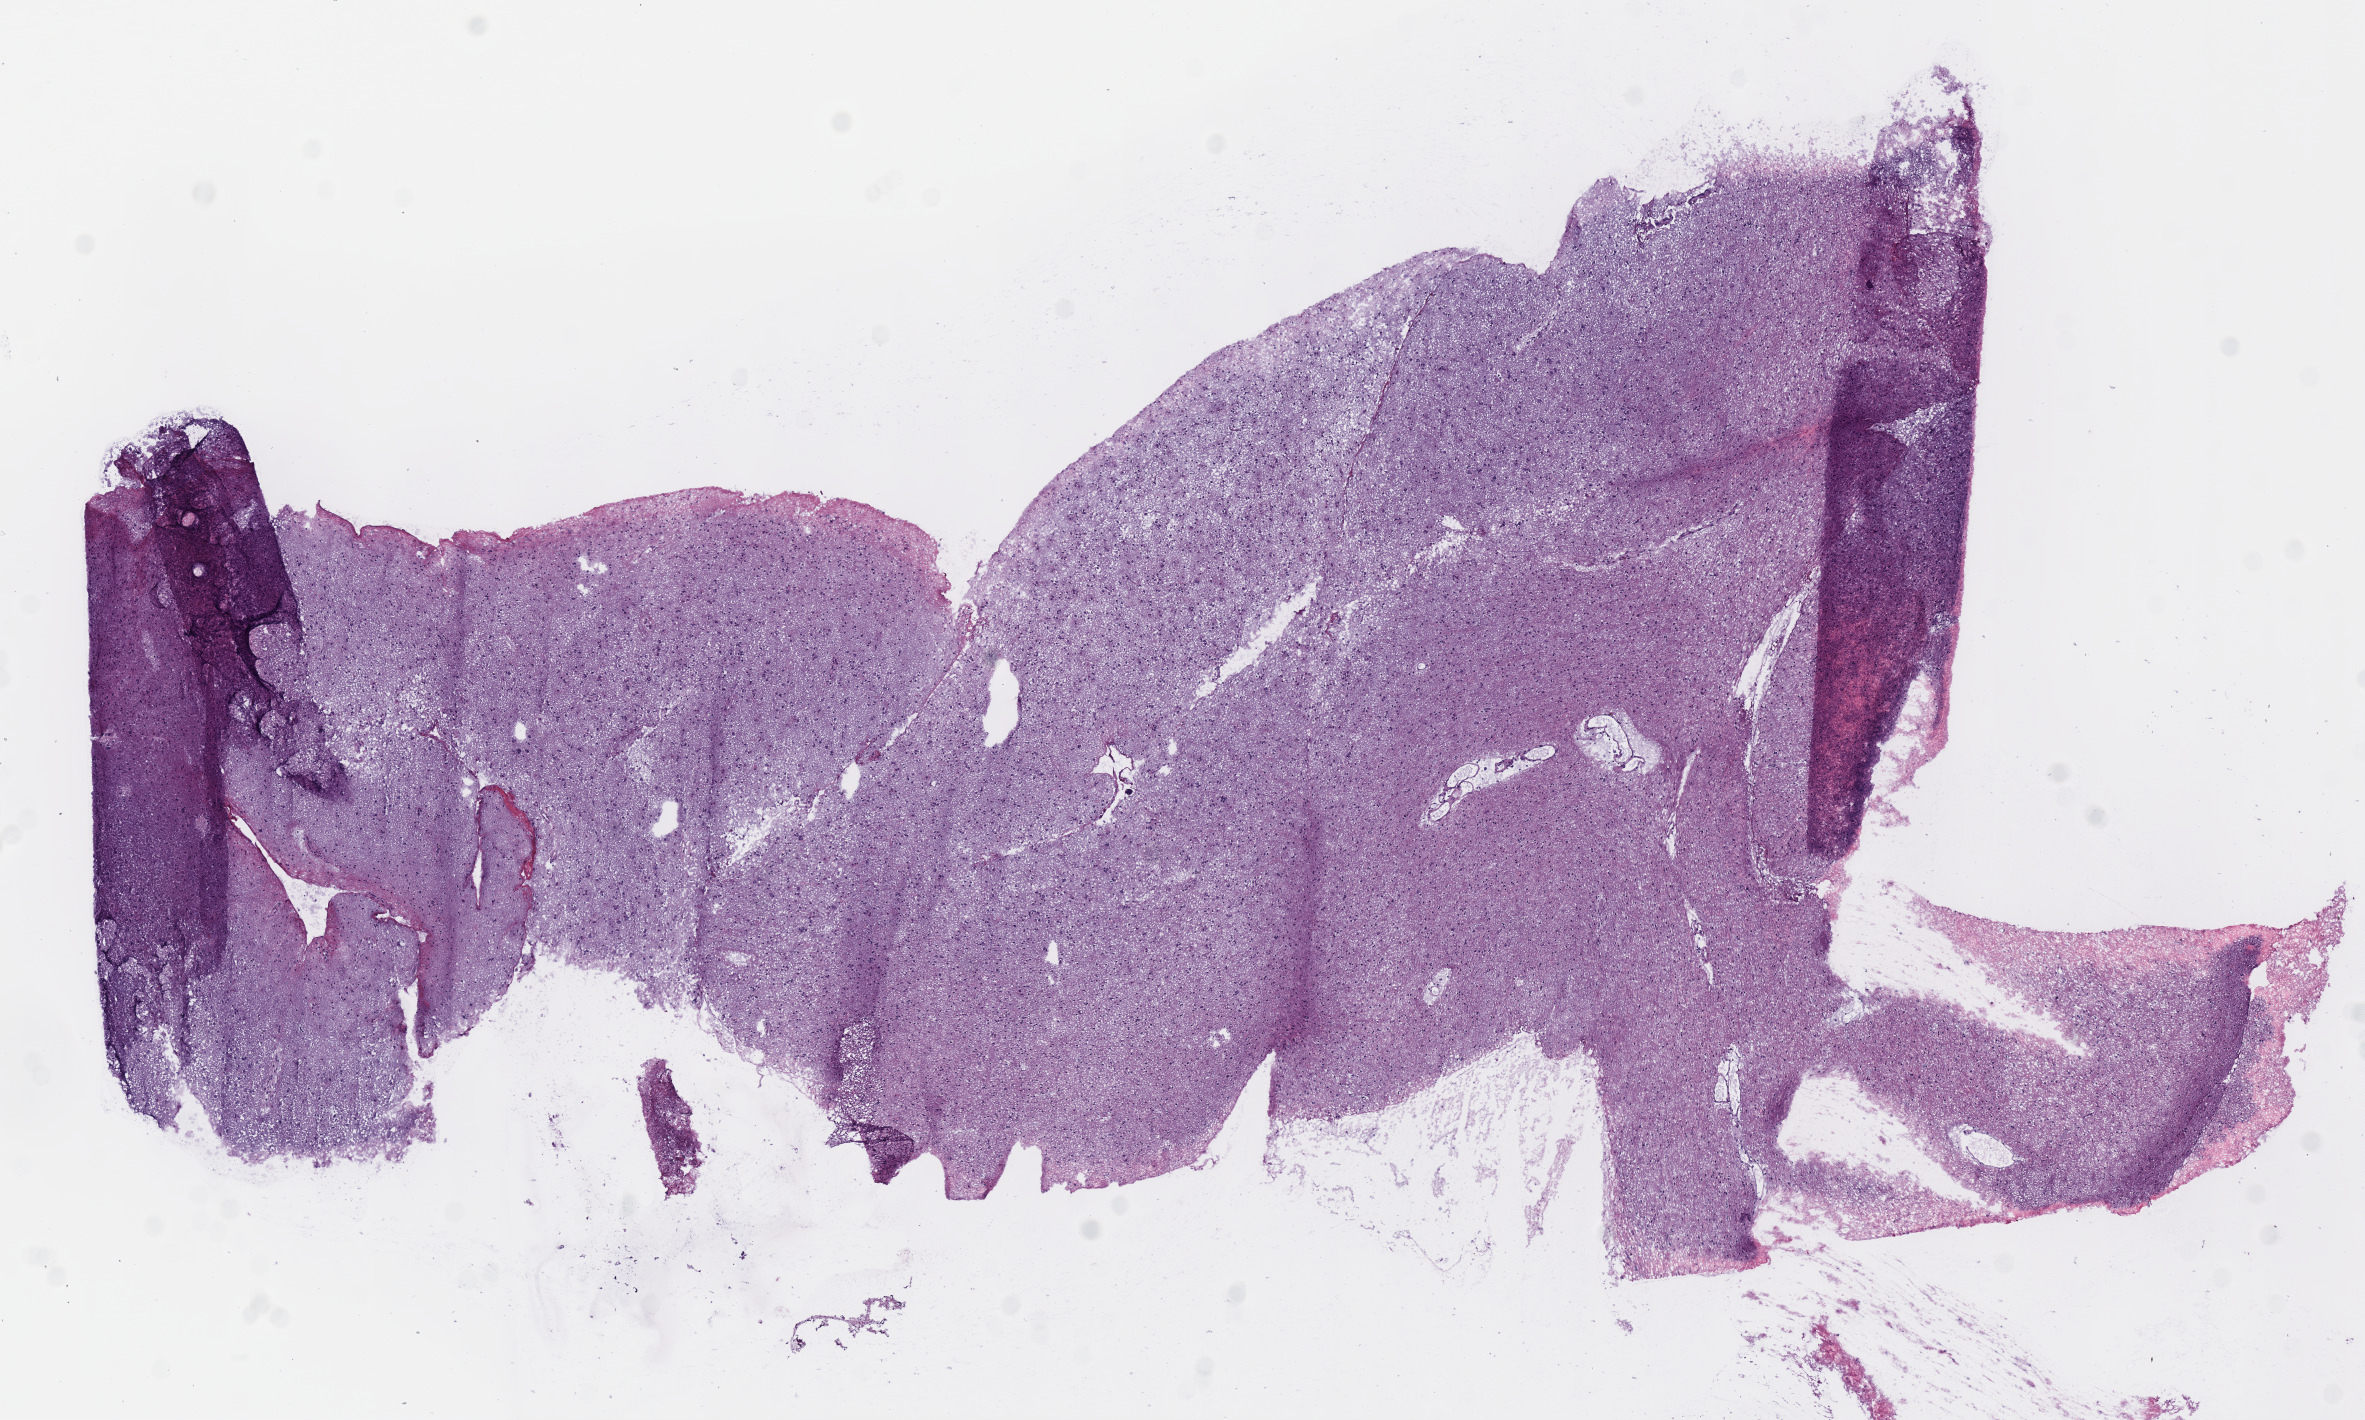
H&E whole-slide image — shown as a low-resolution overview of the whole scanned area (about 9.3 x 5.6 mm), frozen section from the top of the tissue portion, primary tumour sample from the brain. Patient: female, age at initial diagnosis 64 years.
Pathologic diagnosis: Oligodendroglioma, NOS.